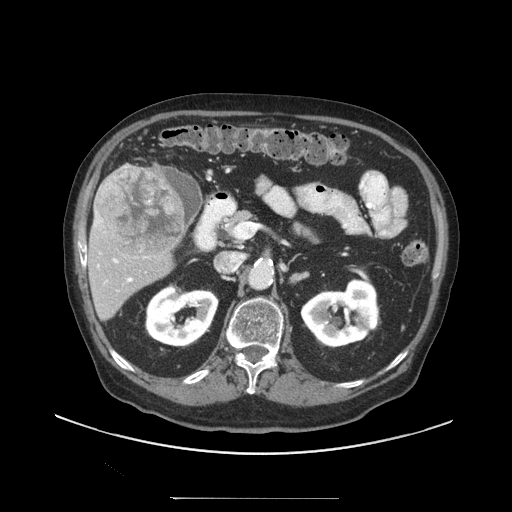
Contrast-enhanced abdominal CT (liver protocol), one axial slice; reconstruction kernel STANDARD; 140 kVp; soft-tissue window (W 400 / L 40 HU); 2.5 mm slice thickness; 512 × 512 image matrix, field of view 450 × 450 mm. From the clinical record (not read from this slice): diagnosis: hepatocellular carcinoma (patient treated with transarterial chemoembolisation; whether this scan precedes or follows treatment is not stated here); TNM stage (as recorded): Stage-IIIC; Child-Pugh class: A; tumour nodularity: uninodular.
Outlined on this slice (semi-automatically segmented with operator editing):
- liver parenchyma outside the tumour (the mass and vessels are separate outlines, so this box may not span the whole liver): box from (x=88, y=164) to (x=194, y=320) px
- mass: (x=97, y=166)–(x=185, y=258)
- liver vessels: (x=94, y=213)–(x=133, y=283)